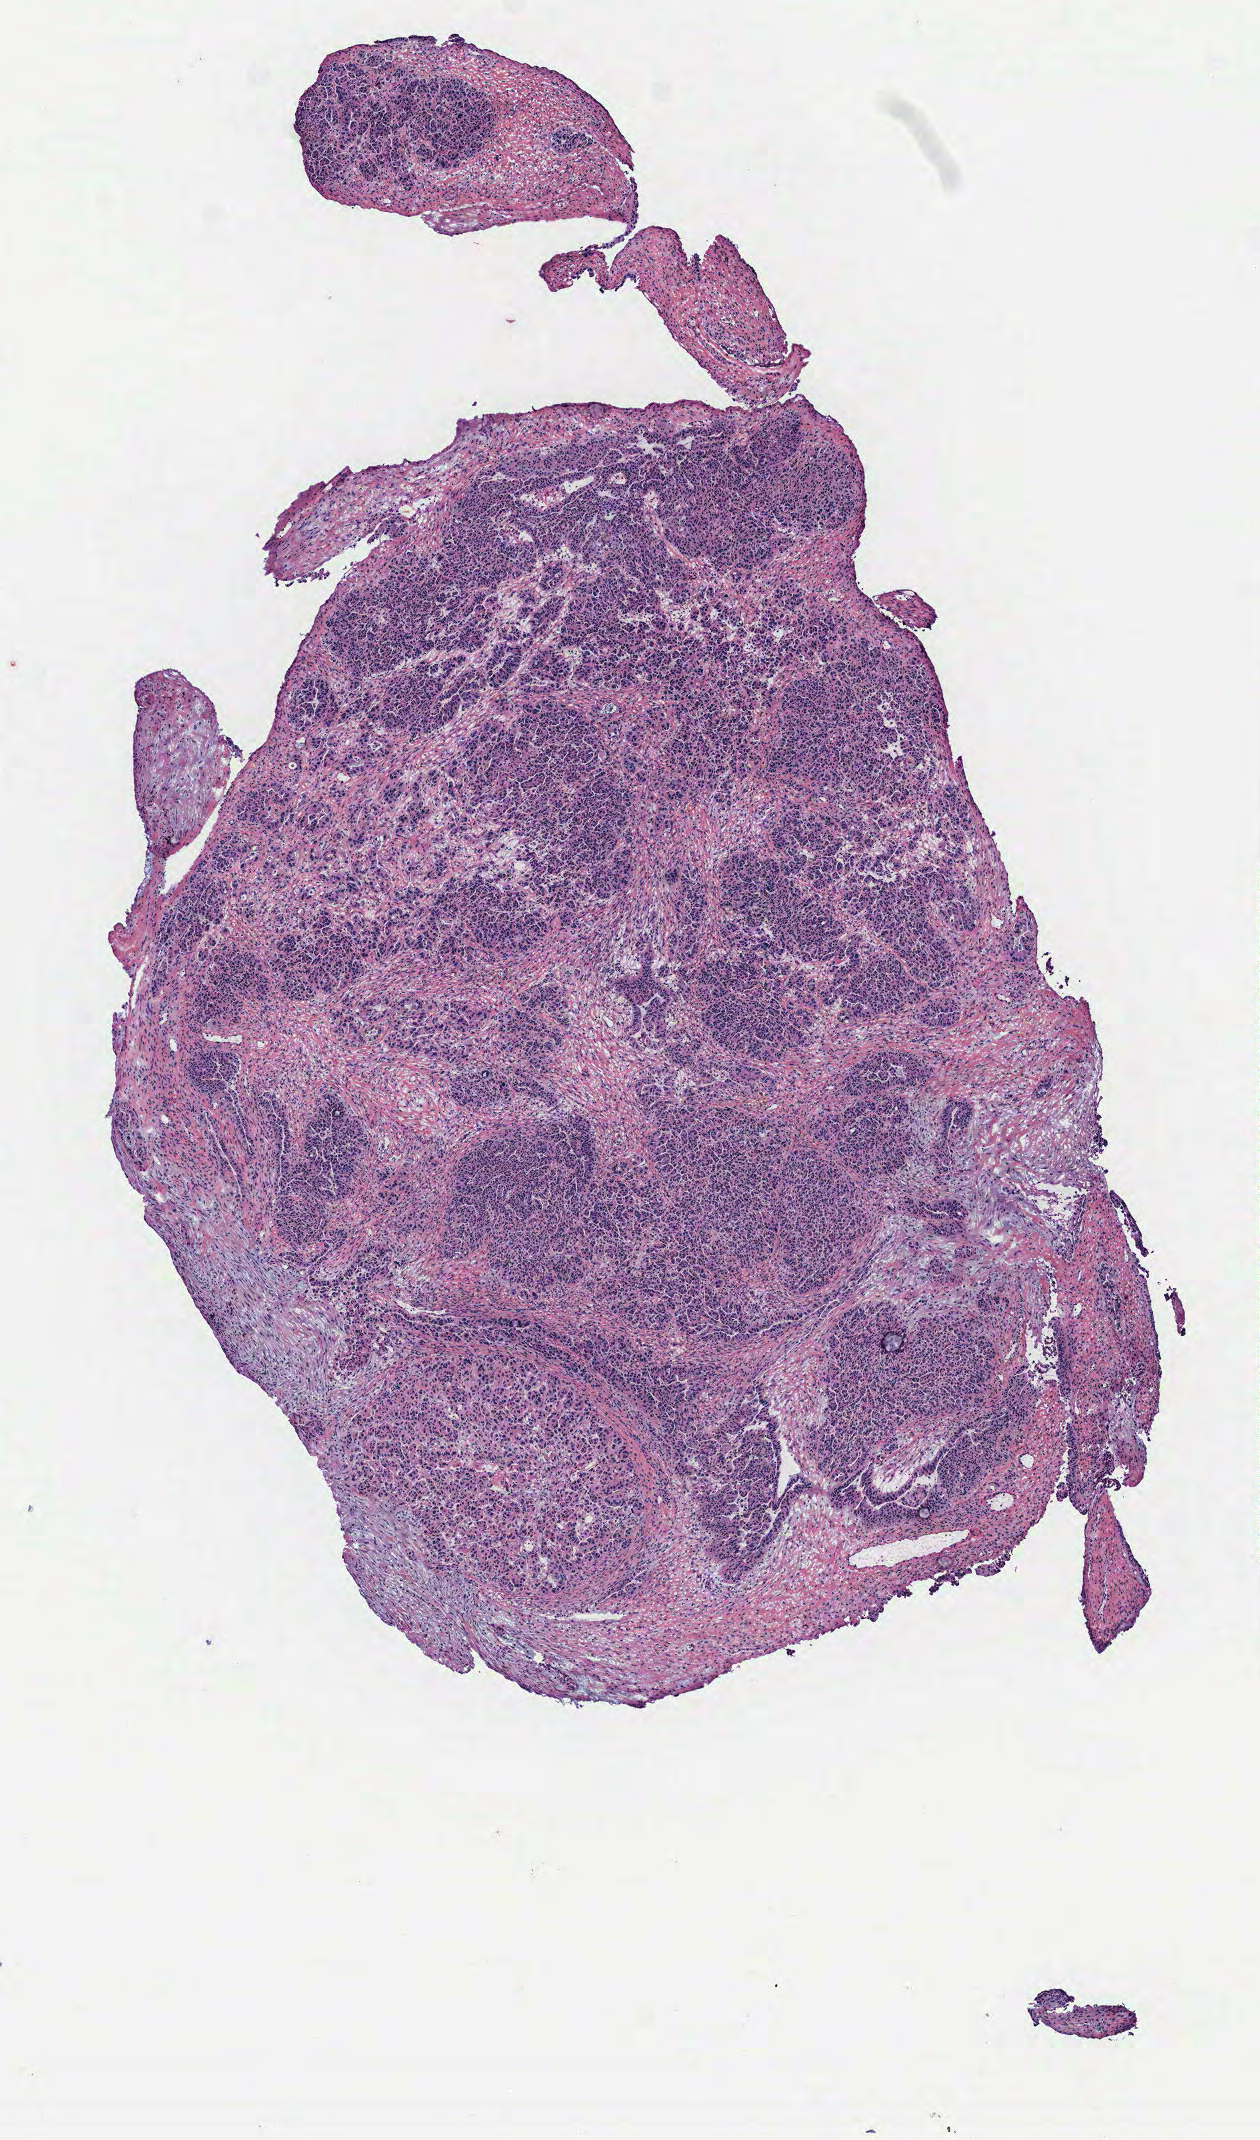
Digitized H&E tissue section (whole slide) — shown as a low-resolution overview of the whole scanned area (about 5.0 x 8.6 mm). Tumour tissue sample, ovary. Female, 58 y/o.
Primary tumour site (as recorded): ovary. Histologic diagnosis: Serous adenocarcinoma, NOS.